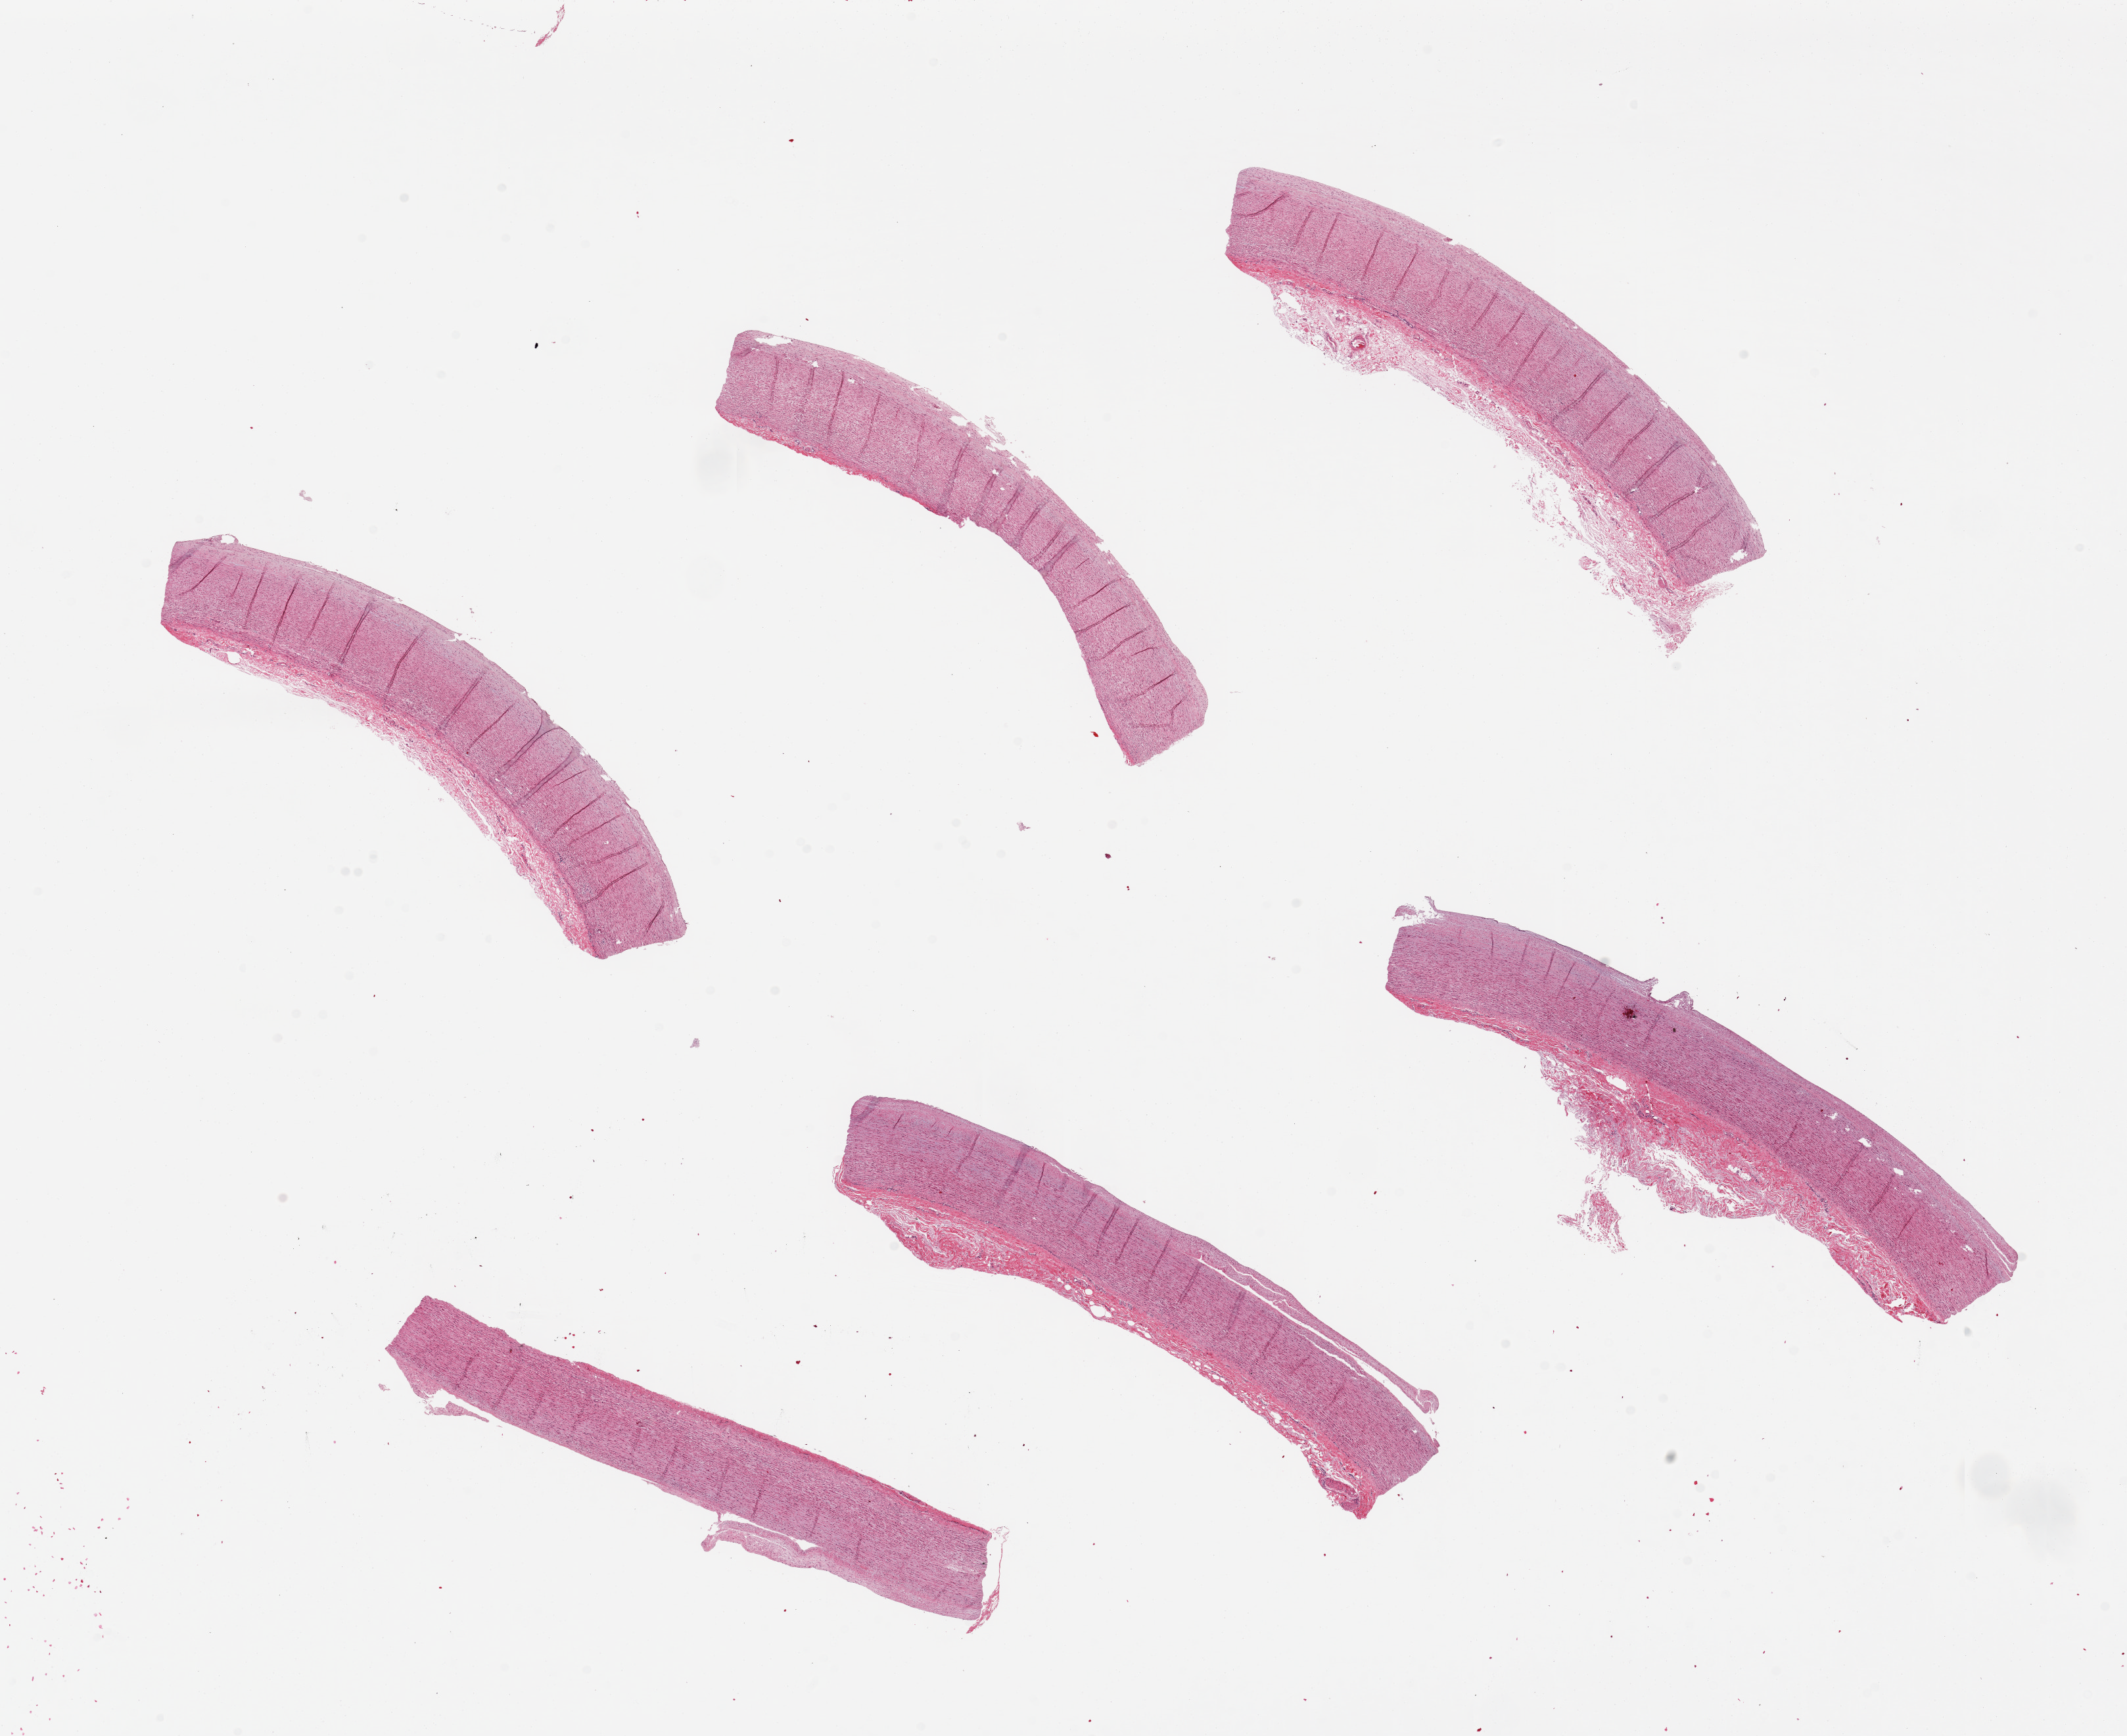
Whole-slide image, haematoxylin and eosin stain — a low-resolution overview of the entire scanned area, about 25.6 x 20.9 mm, PAXgene-fixed, paraffin-embedded tissue, section of aorta (target tissue), donor tissue sample. Donor sex: female.
* reviewer comment on this tissue sample: 6 pieces, up to 9x3mm; adherent adventia up to ~1mm along edges of most sections